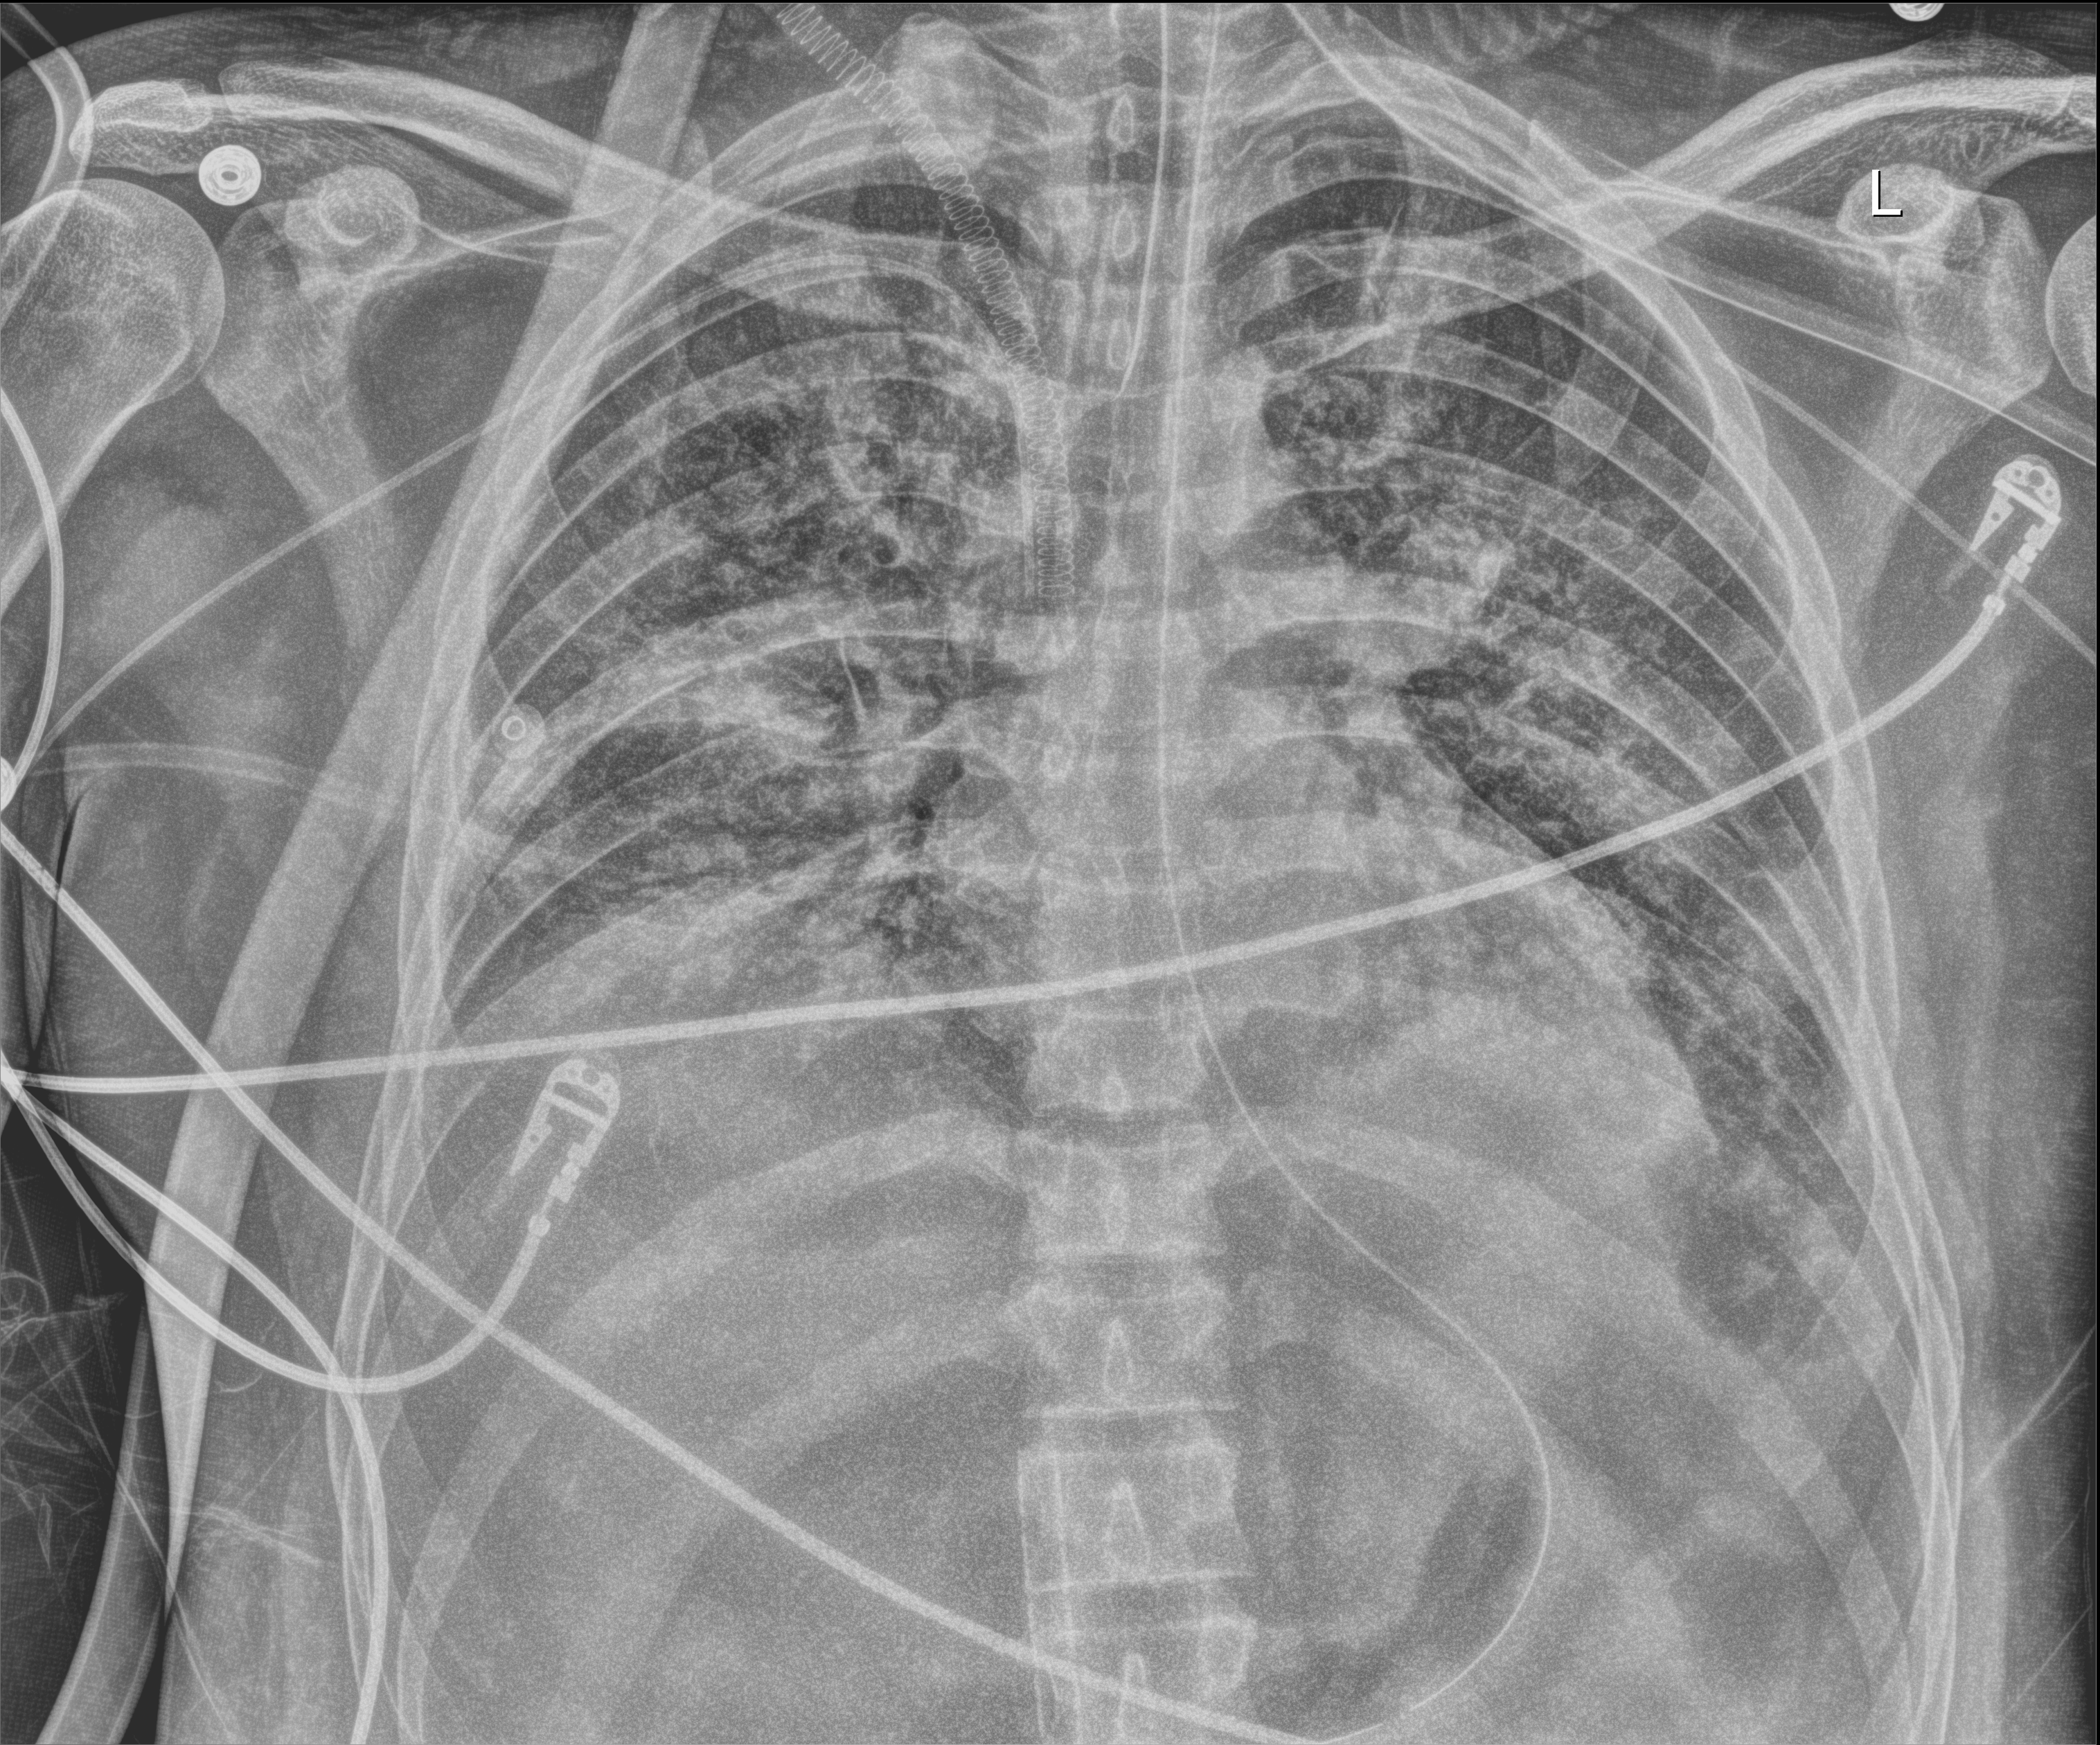
Chest radiograph, anteroposterior (AP) projection. Adult patient hospitalised with COVID-19, age 18–59 years.
Admission-level facts for this patient (not findings on this image; timing relative to this image not recorded): admitted to intensive care during this hospital stay: yes.